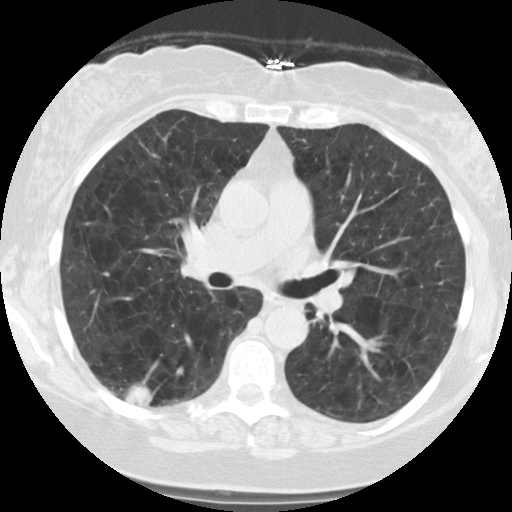
Low-dose screening chest CT, axial slice, second screening round (one year after baseline), lung window (W 1500 / L -600 HU), 2.5 mm slice thickness, slice 56 of 122 in the series, 512 × 512 image matrix, field of view 310 × 310 mm. Female, age 59 years at enrolment. Current smoker at enrolment.
Expert-annotated lung lesion, bounding box <106,359,174,419> (left, top, right, bottom; pixels). The screening reader recorded 2 non-calcified nodules or masses ≥4 mm on this exam; which of them this box marks is not recorded. Official screen result: positive, other. Participant outcome: lung cancer diagnosed 63 days after this screen — squamous cell carcinoma, NOS, right lower lobe, poorly differentiated (G3), stage IB (AJCC 6th edition), 30 mm at pathology.